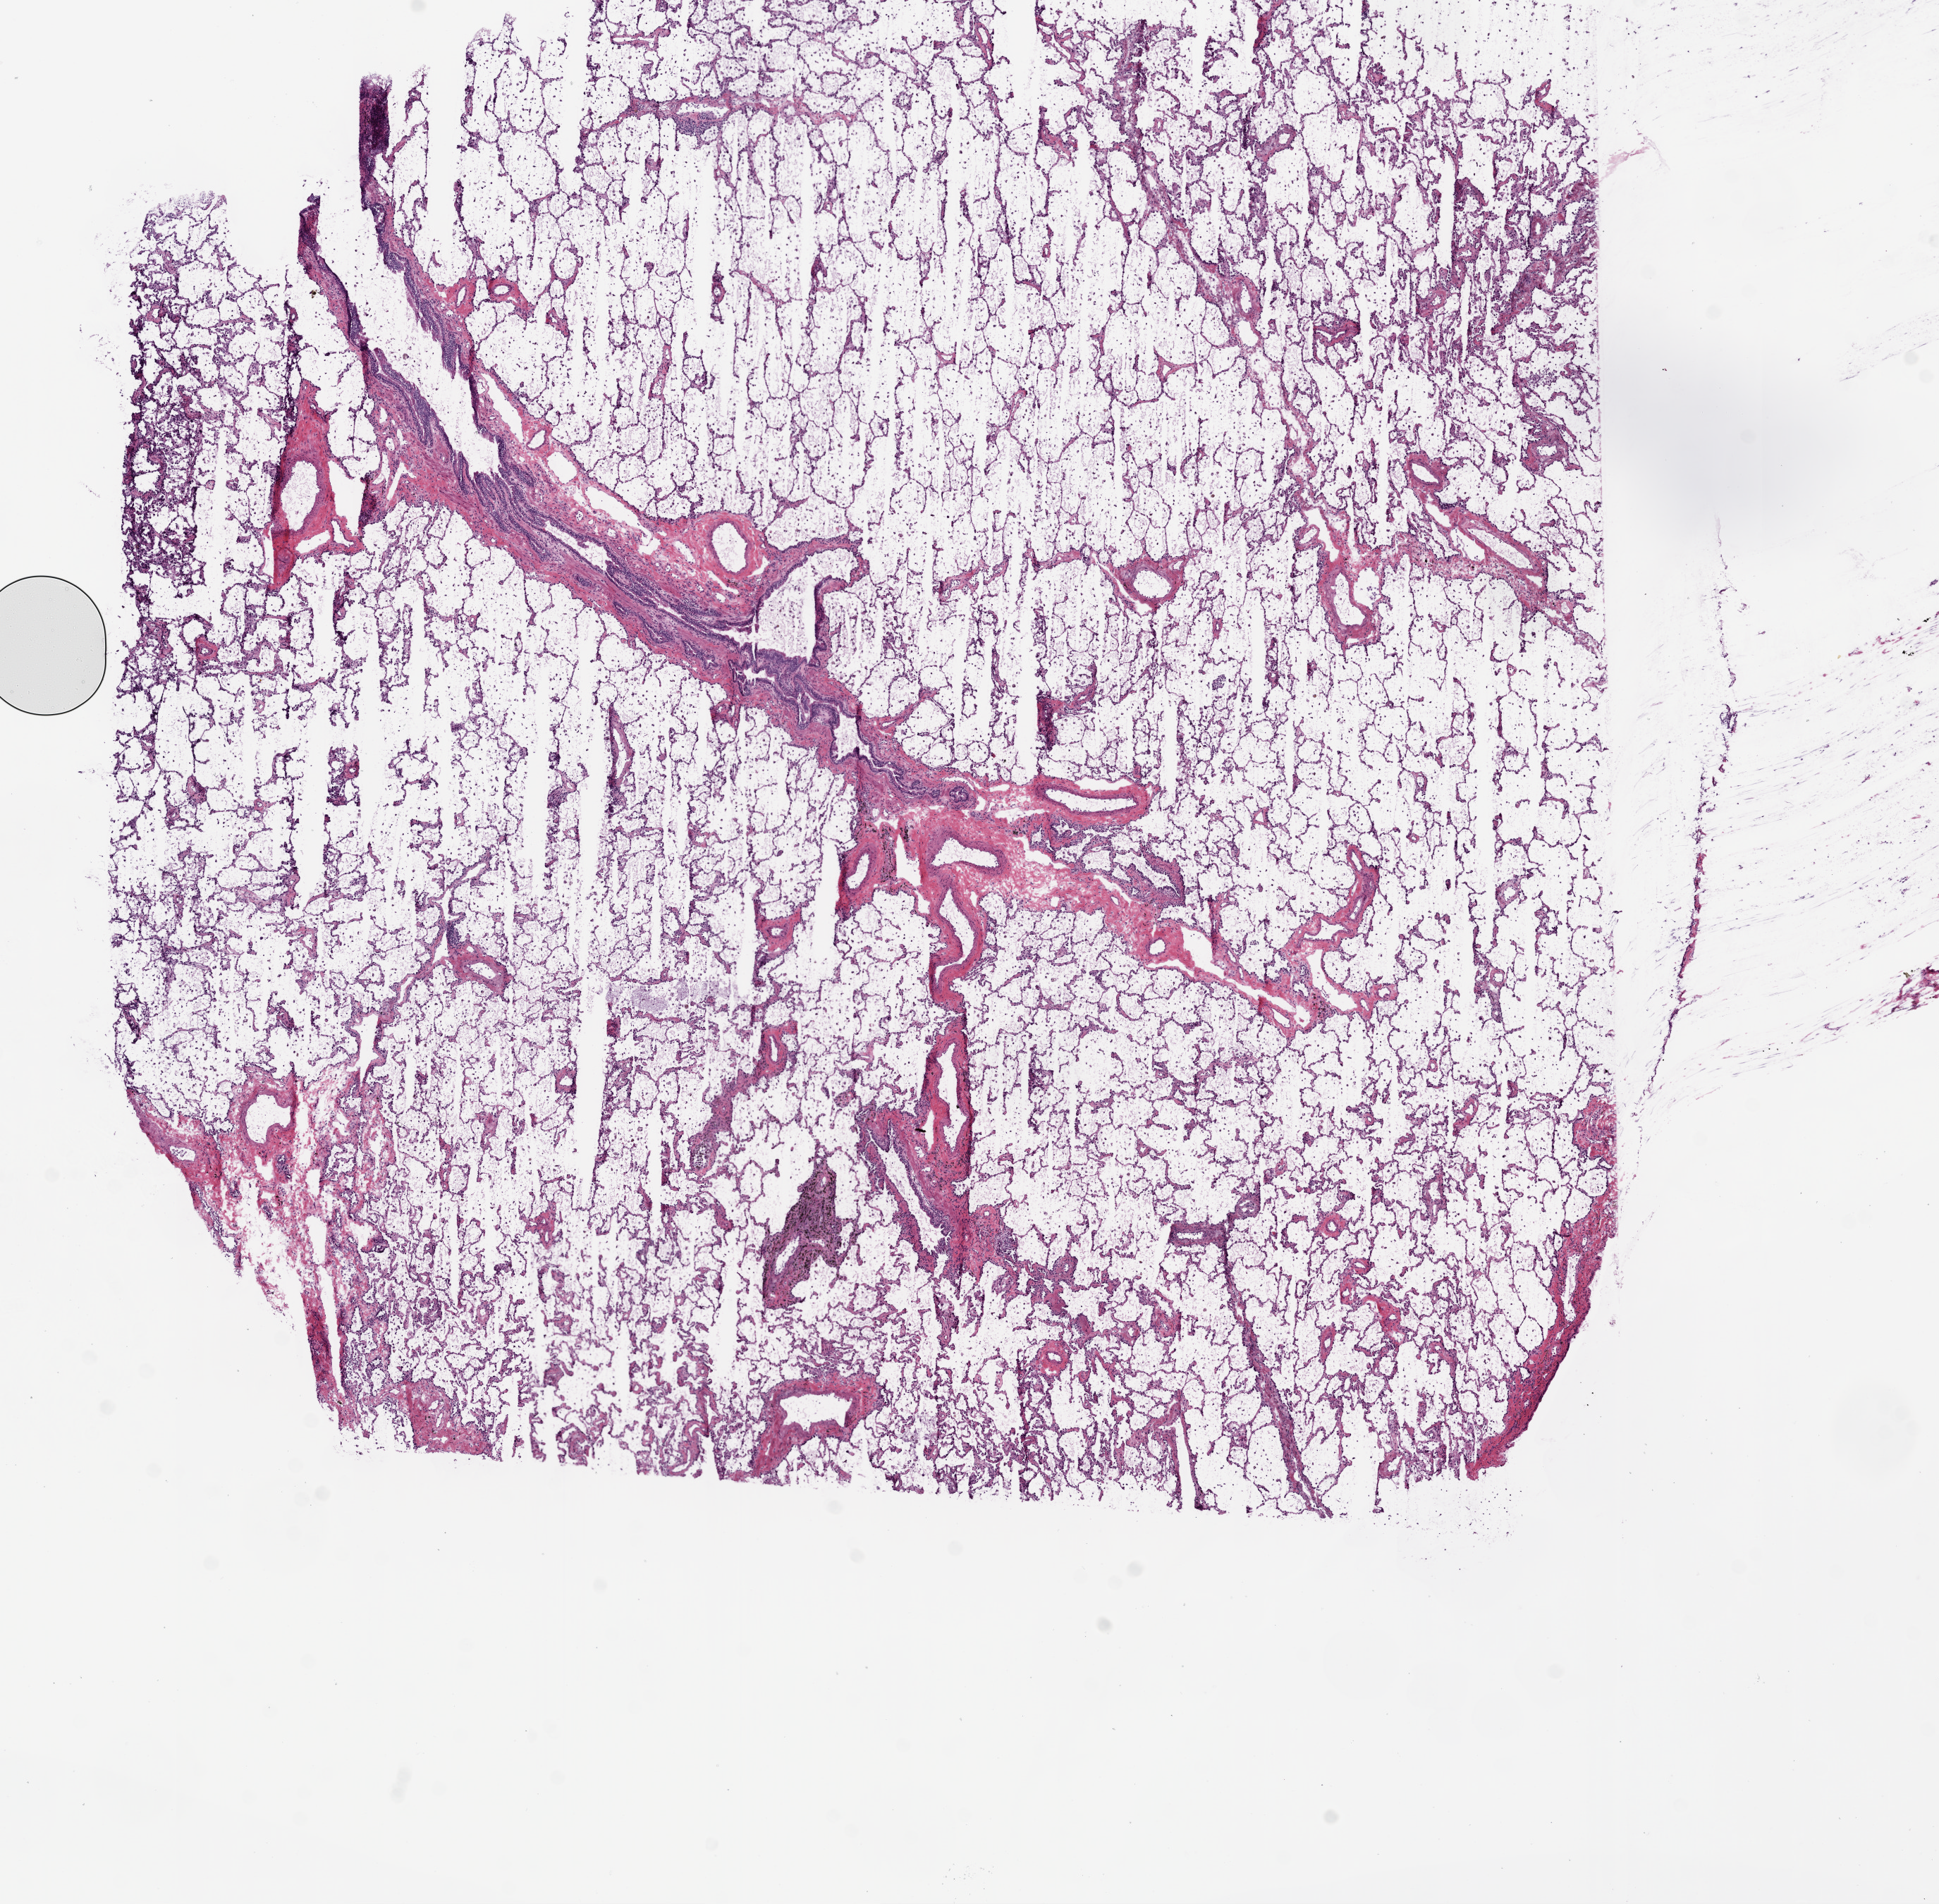
Whole-slide histology image, Hematoxylin and eosin (H&E) stained — a low-resolution overview of the entire scanned area, about 11.0 x 10.8 mm. Frozen section. Lung, solid tissue normal (non-tumour tissue) sample. Male patient; age at initial diagnosis 42 years.
This section: solid tissue normal sample (biorepository sample class). Patient diagnosis: Adenocarcinoma, NOS.